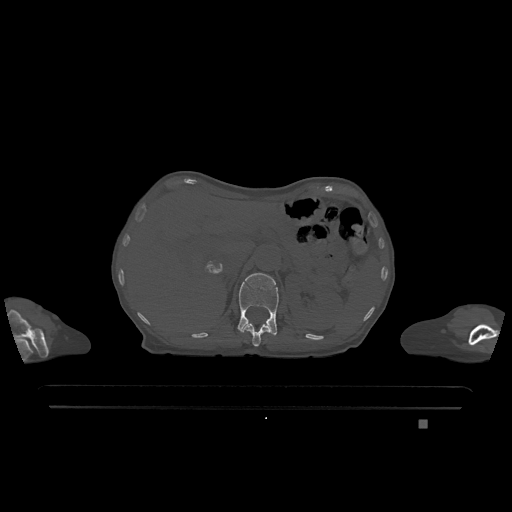
CT including the spine, one axial slice; slice 496 of 1317 in the series (ordered by position); bone window (W 1800 / L 400 HU); 0.5 mm slice thickness; 512 × 512 image matrix, field of view 500 × 500 mm. Female patient, age 74 years. From the clinical record (not read from this slice): primary cancer: lung.
Structures marked on this image (semi-automatically segmented with operator editing):
- L1 vertebra: bounding box [x1, y1, x2, y2] px = [238, 273, 279, 336]
- T12 vertebra: [241, 324, 270, 347]